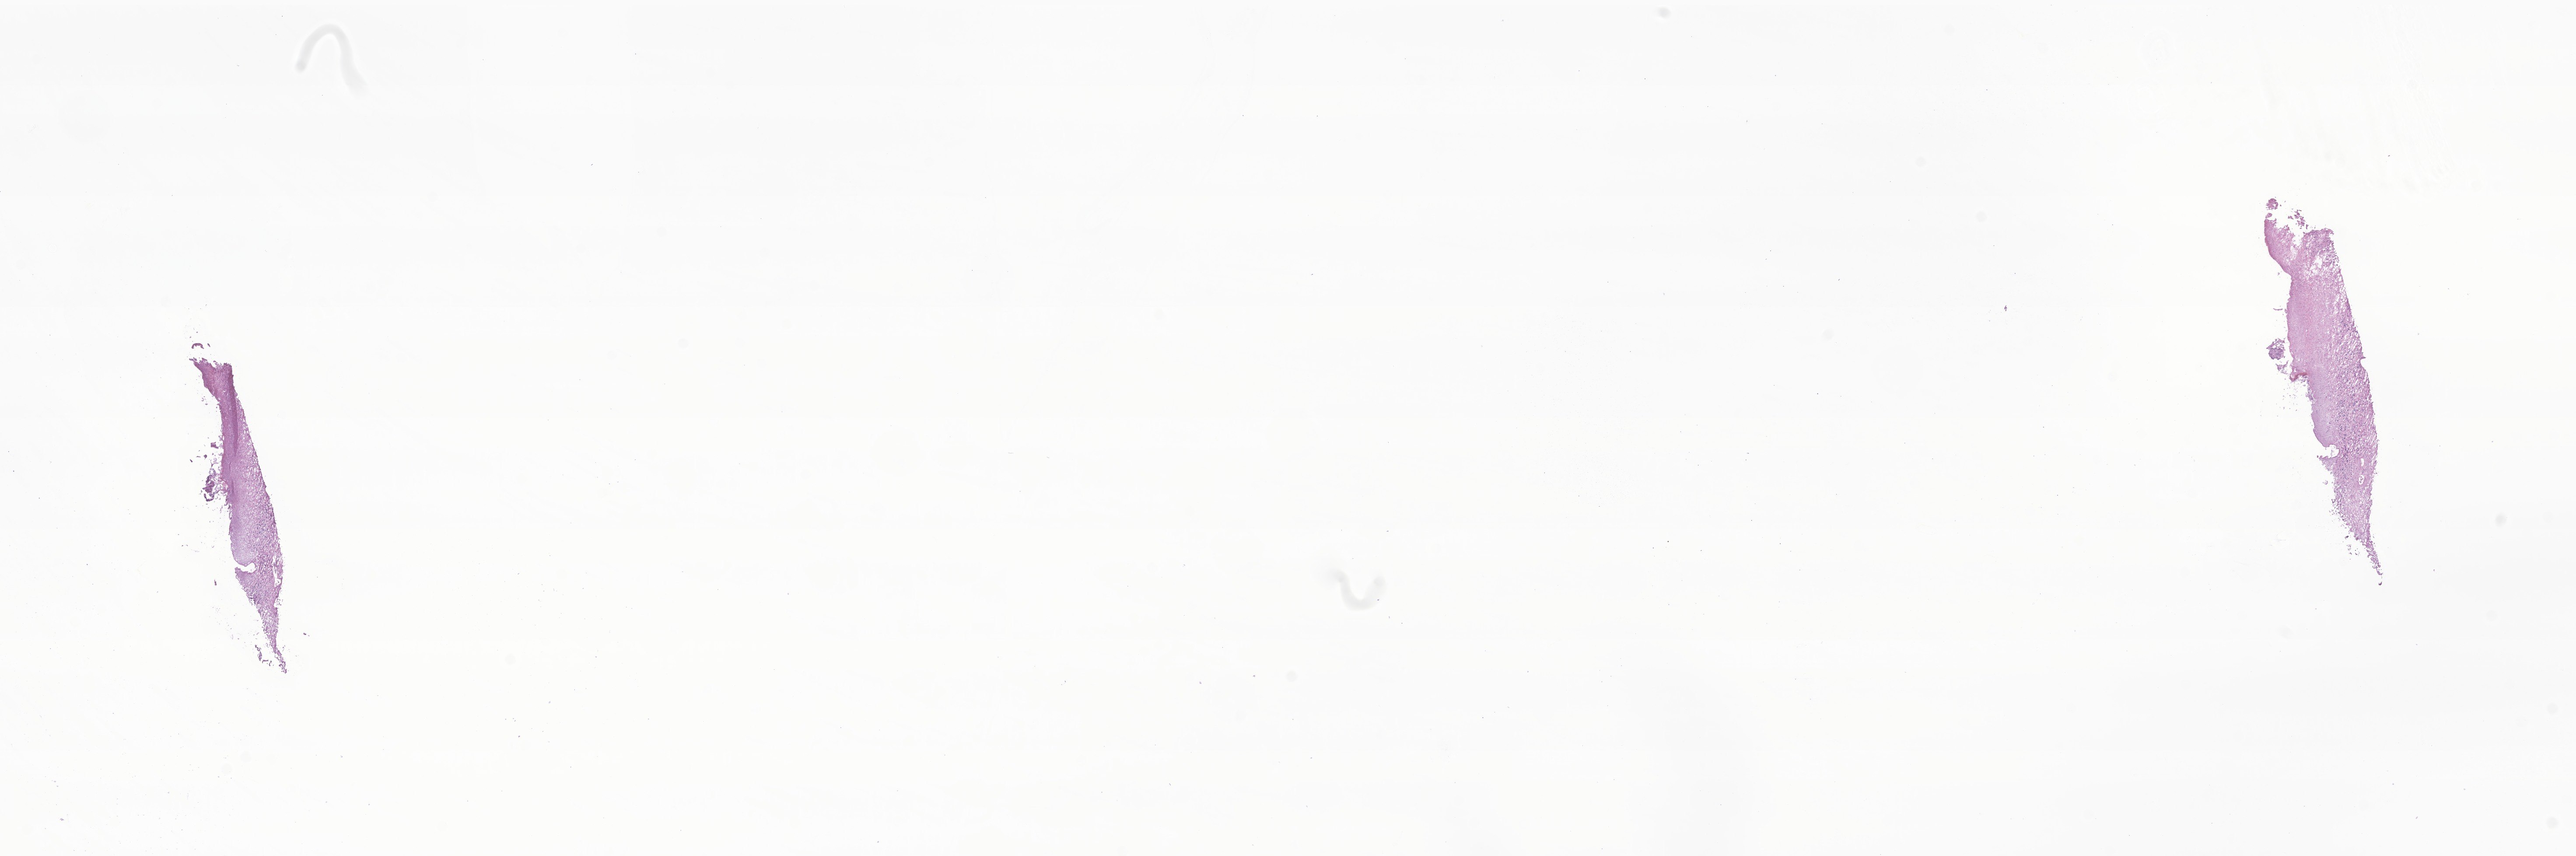
Whole-slide image, H&E stain of tumor tissue from the brain — whole scanned area (about 24.8 x 8.2 mm) shown as a low-resolution overview. Frozen section. Patient female; age 153 months.
* recorded diagnosis: Glioma, malignant